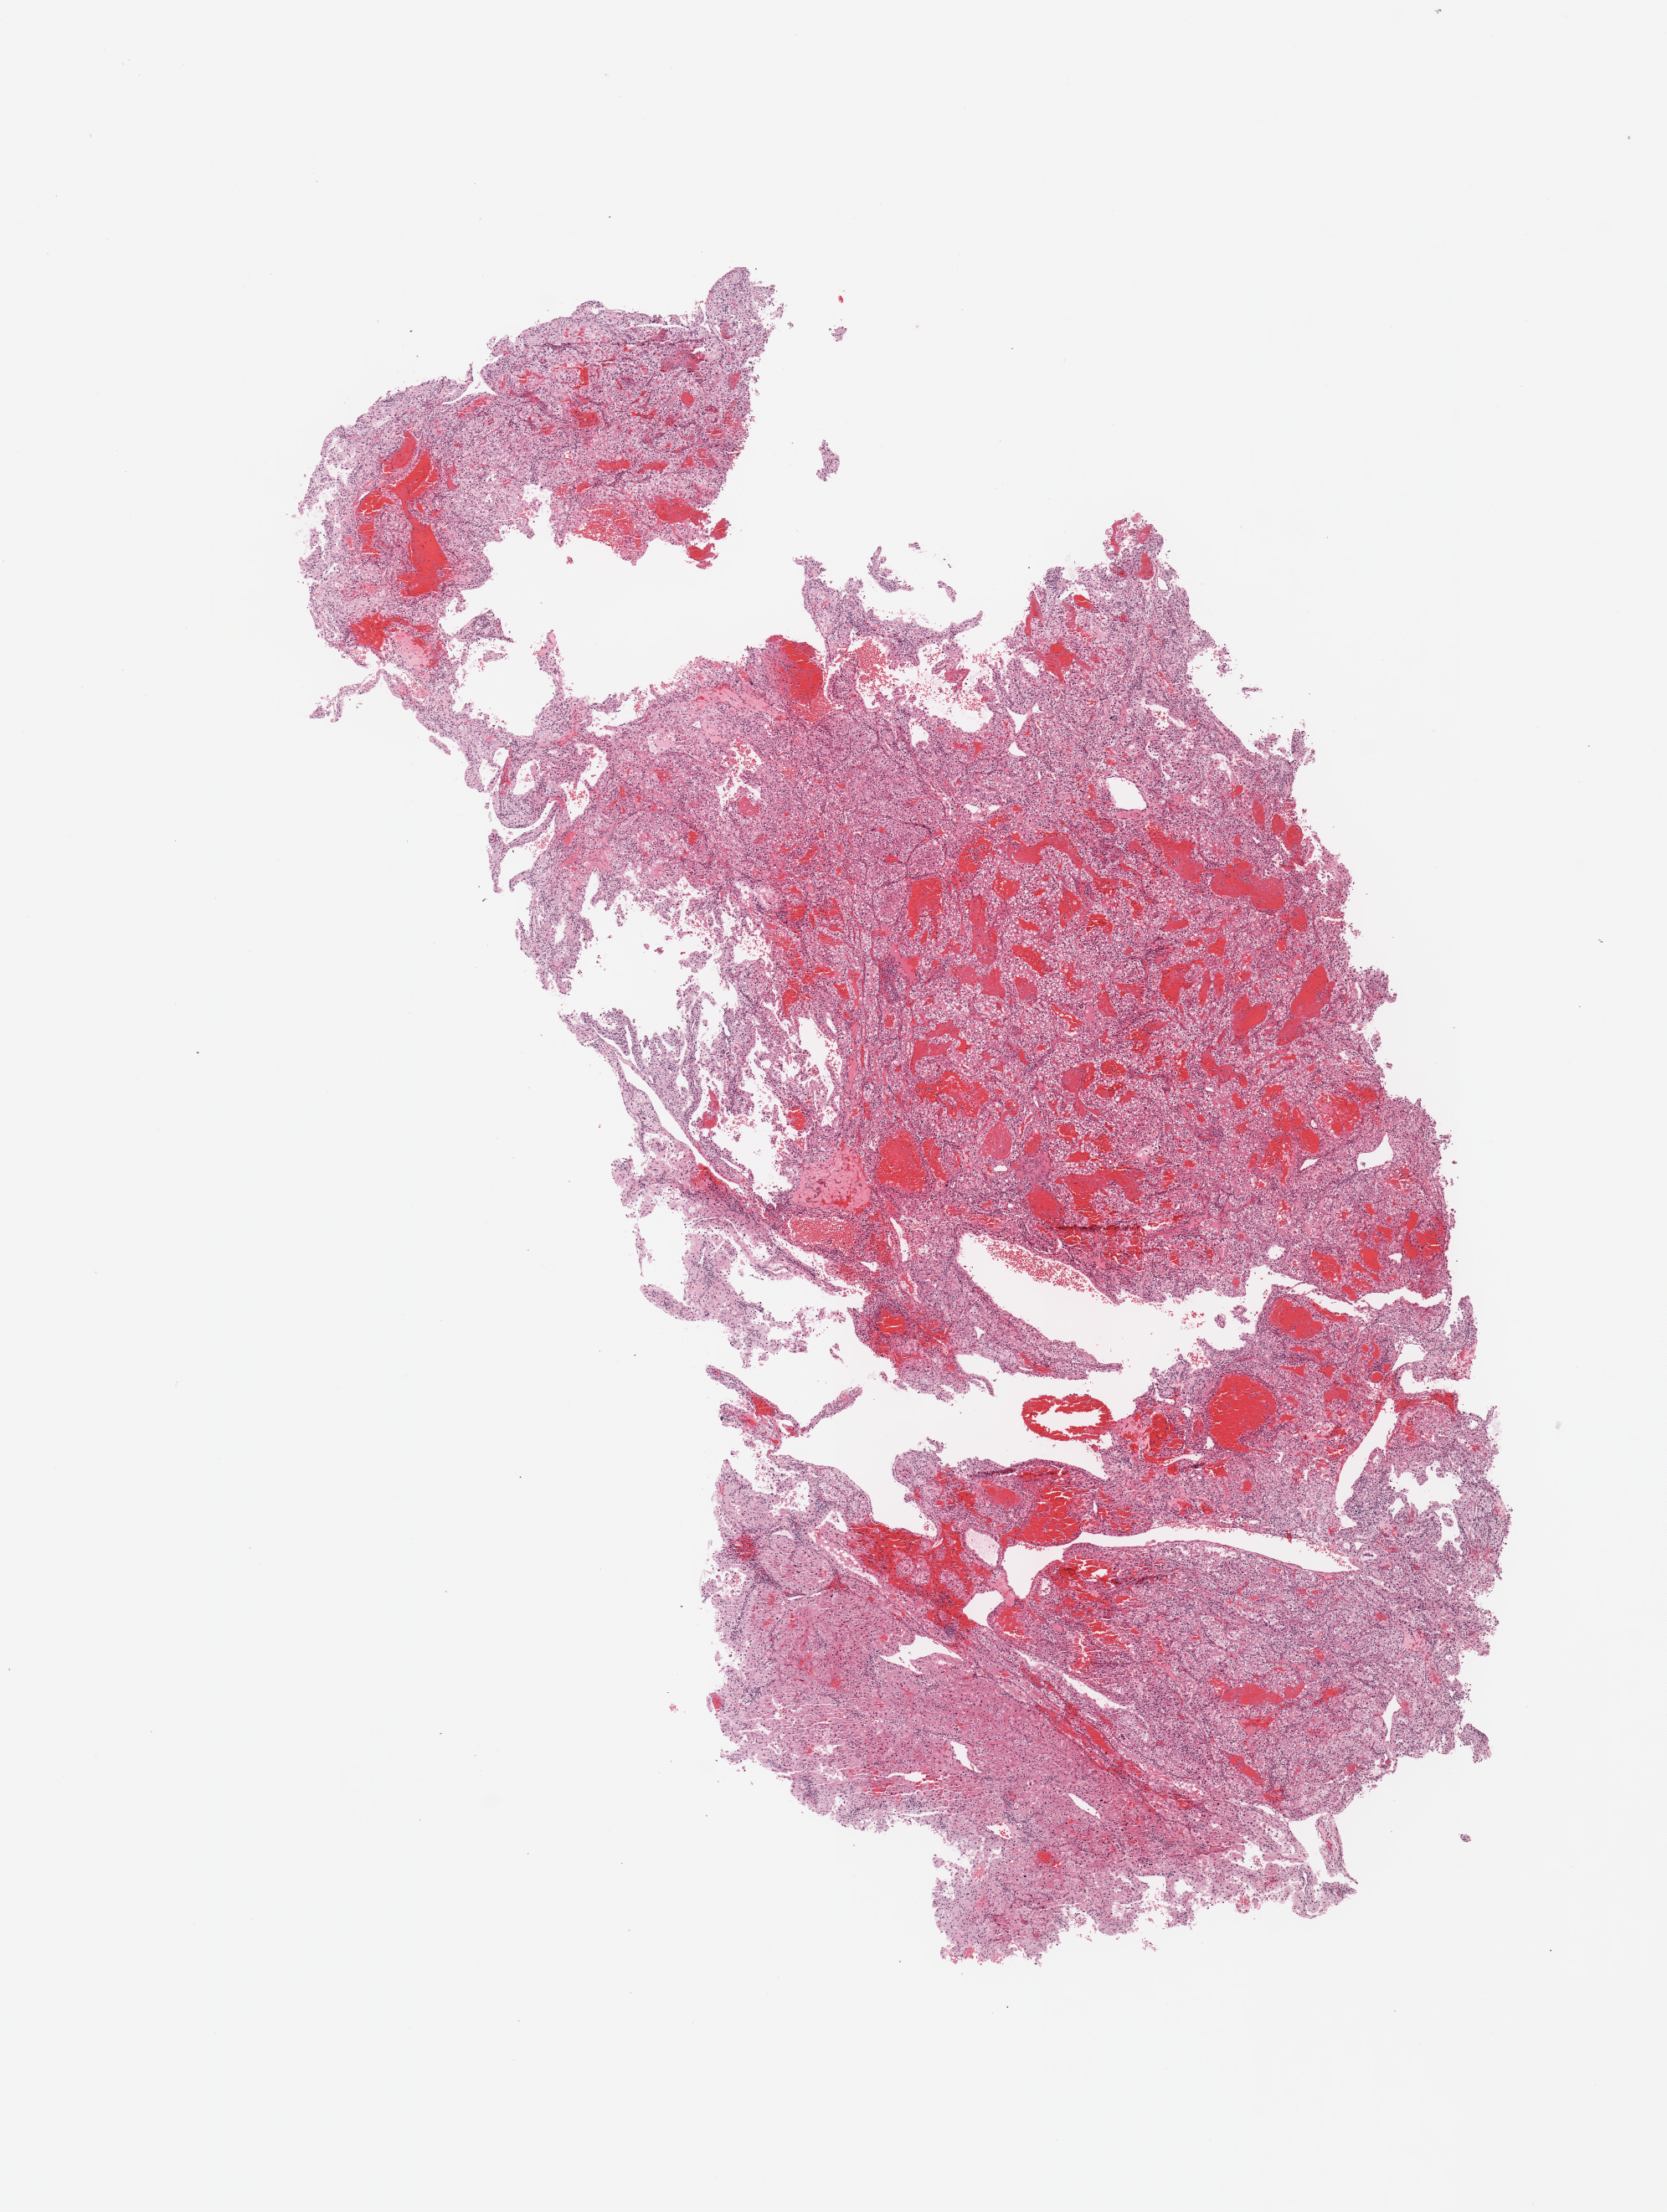
H&E whole-slide image — whole scanned area (about 7.9 x 10.5 mm, from a 20x scan) shown as a low-resolution overview, tumour tissue sample, sampled site: kidney. Female patient, aged 90 or older. Histologic grade: G3 (poorly differentiated). Pathologist review of this section (percent, as recorded): tumour nuclei 80%, necrosis 10%.
Primary tumour site (as recorded): lower pole. AJCC pathologic stage: II. Diagnosis: Renal cell carcinoma, NOS.